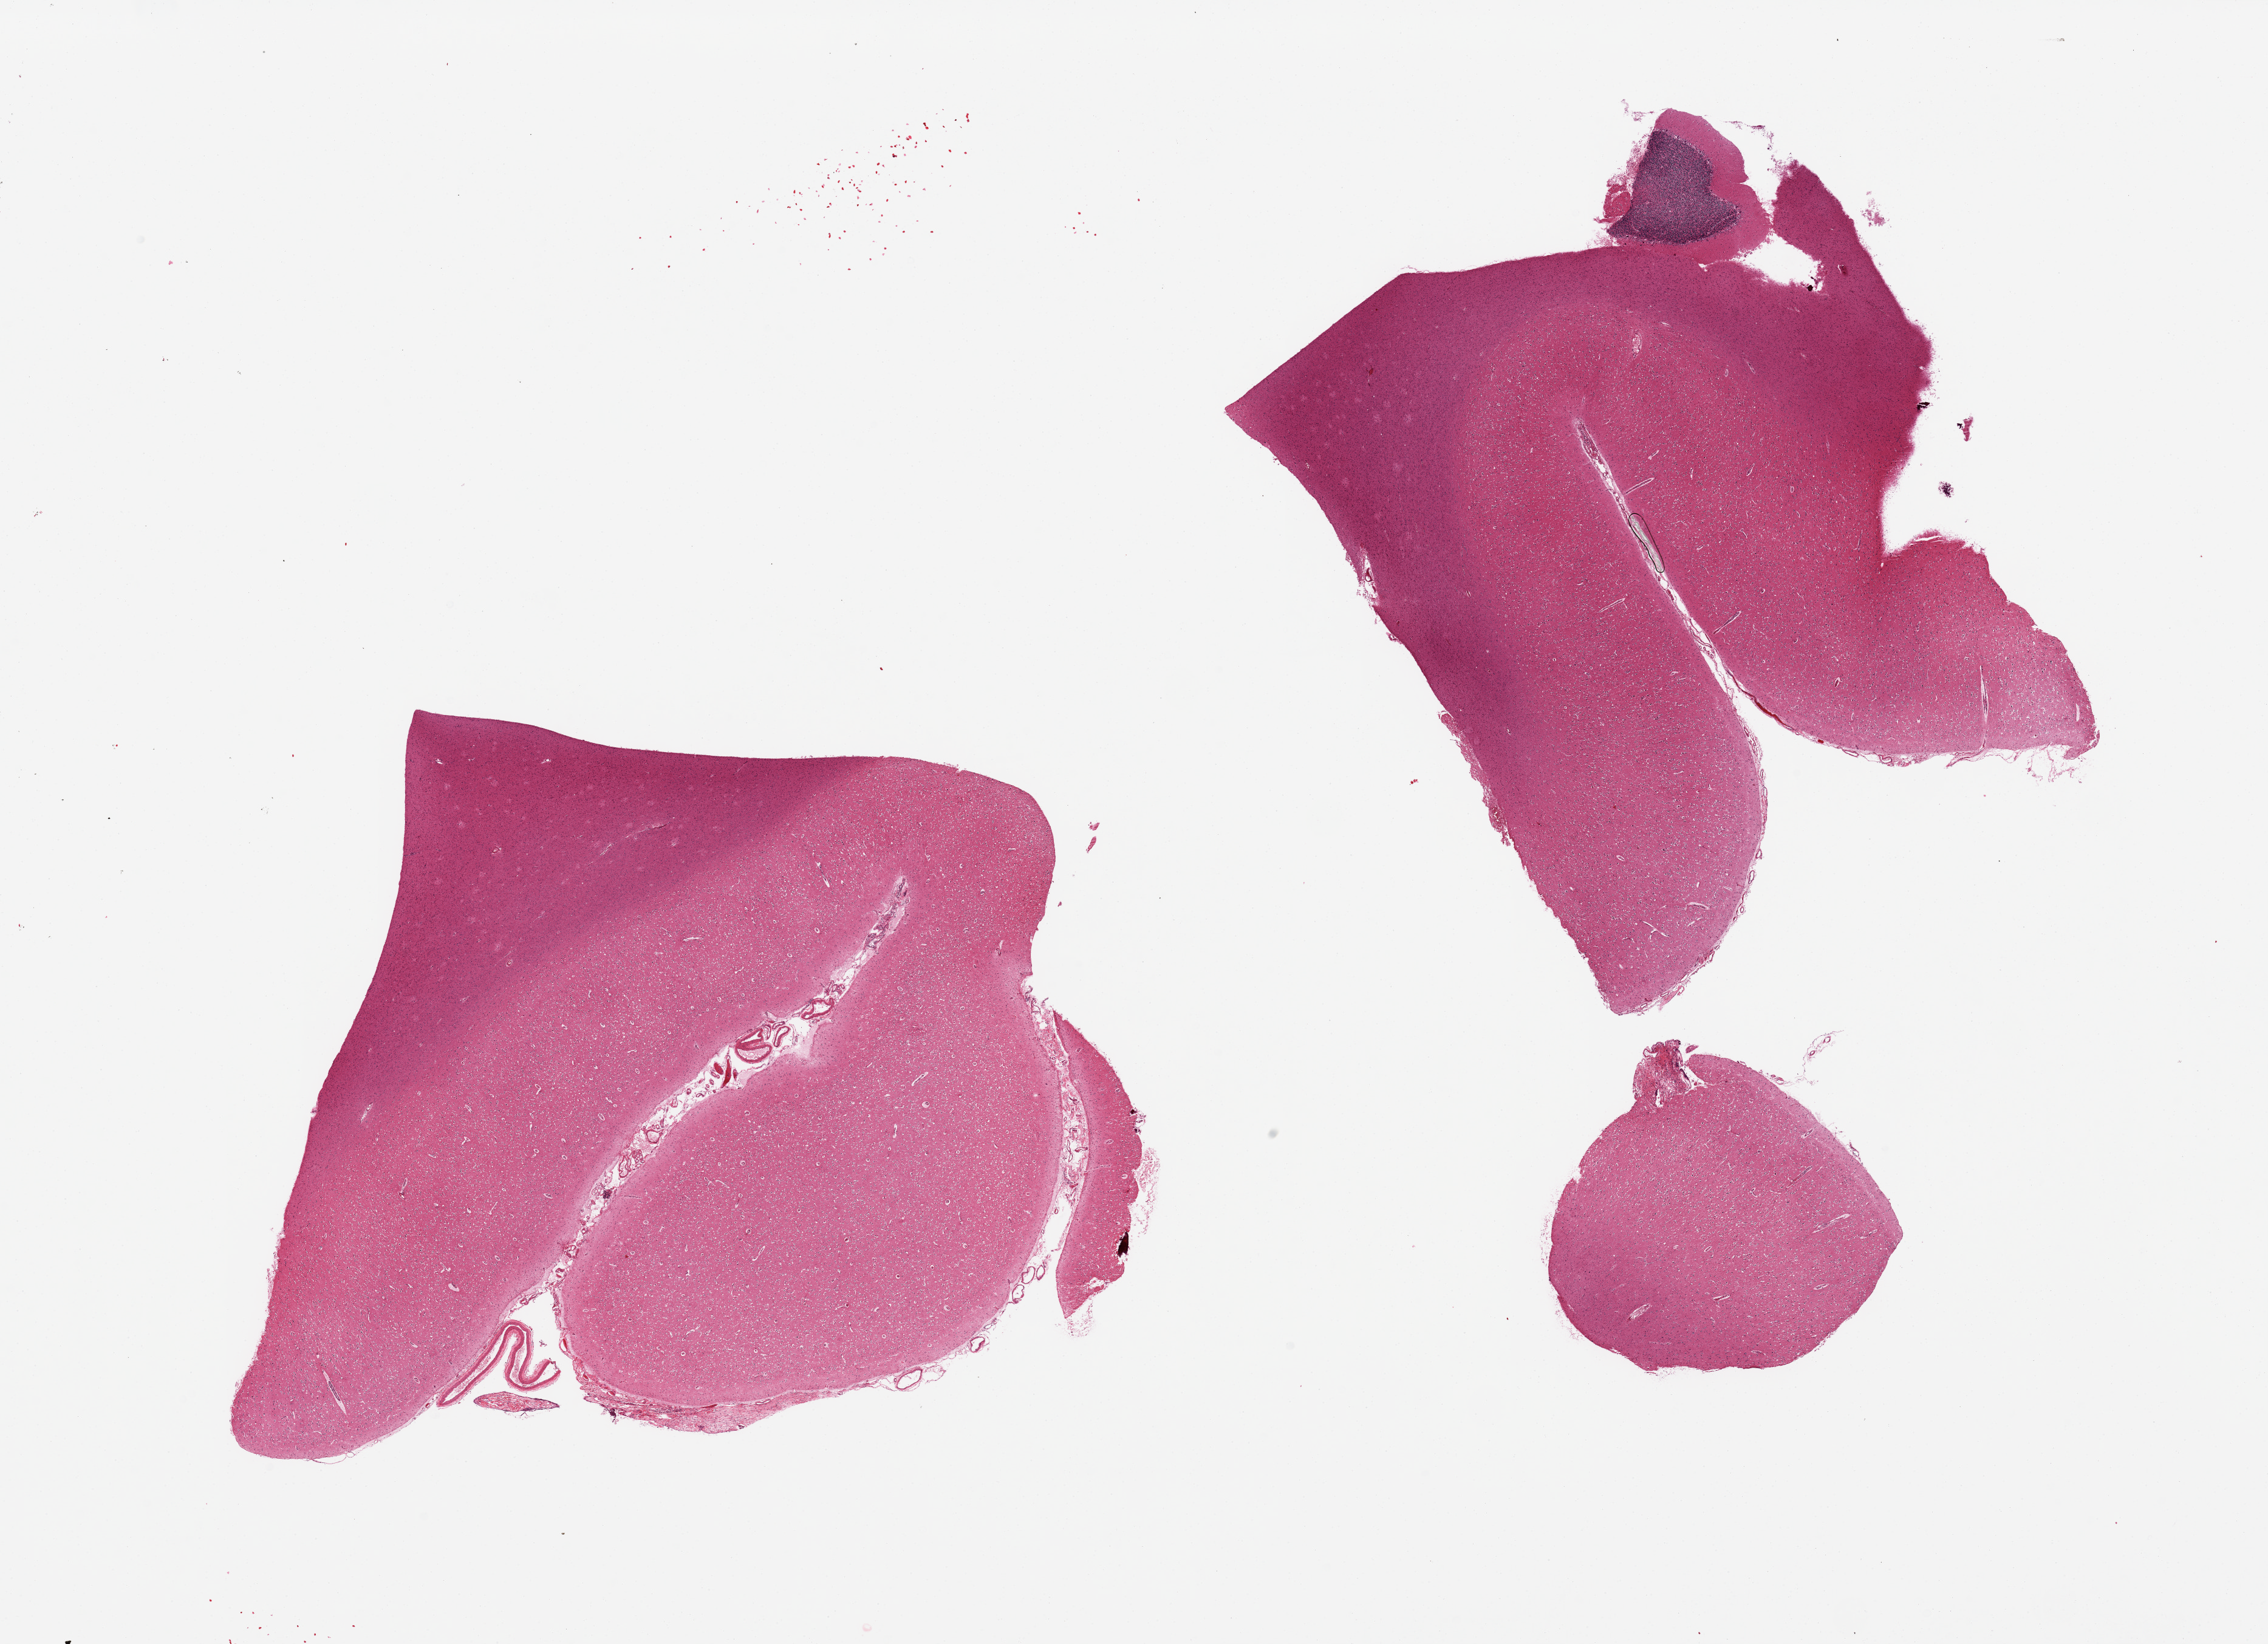
H&E whole-slide image — a low-resolution overview of the entire scanned area, about 29.5 x 21.4 mm (acquisition: 20x scan); PAXgene-fixed paraffin-embedded (PFPE) section; section of cerebral cortex (target tissue); tissue donor sample. Donor: male.
Pathologist's review note for this sample: 3 pieces , includes small detached fragment of cerebellum.